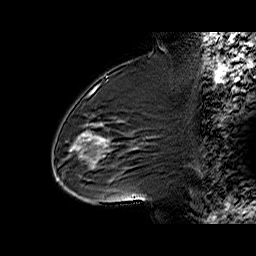
Breast MRI (dynamic contrast-enhanced), one sagittal slice; slice 34 of 60 in the series (ordered by position); dynamic contrast-enhanced series, time point 2 of 6 at this slice position (early post-contrast); 1.5 T; TE 6.3 ms, TR 32.4 ms; 4 mm slice thickness; 256 × 256 image matrix, field of view 200 × 200 mm. Female patient. Case-level facts recorded for this patient, not image findings: setting: breast cancer imaged before/during neoadjuvant chemotherapy; receptor status: triple-negative.
Structures marked on this image (semi-automatic segmentation, software-assisted and operator-edited):
- analysis volume of interest (the breast-tissue region the enhancement analysis was run in; not a lesion): box from (x=65, y=88) to (x=138, y=187) px
- tumour enhancement mask (voxels above the 100 % enhancement threshold inside the analysis volume of interest): (x=76, y=123)–(x=108, y=164)